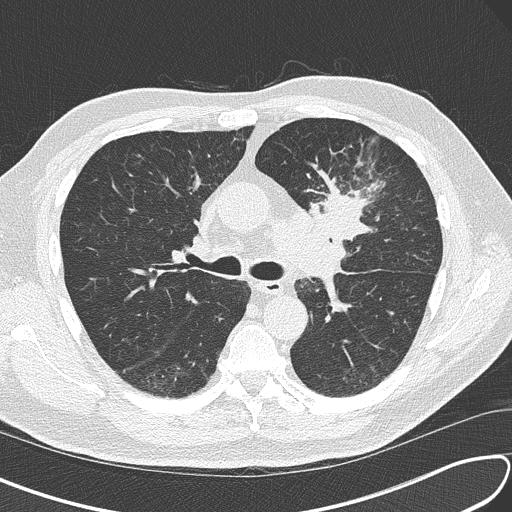
Axial slice from a low-dose chest CT screening exam, third screening round (two years after baseline), lung window (W 1500 / L -600 HU), 2 mm slice thickness. Male, age 67 years at enrolment. Current smoker at enrolment.
Lesion marked by an expert reader, bounding box <296,168,397,261> (left, top, right, bottom; pixels). Screening reader's record for this exam (one nodule recorded; not confirmed to be the boxed lesion): non-calcified nodule or mass ≥4 mm, left upper lobe, 30 × 23 mm, soft tissue attenuation, pre-existing on the prior screen: no. Official screen result: positive, other. Later outcome: lung cancer diagnosed 41 days after this screen — small cell carcinoma, NOS, left upper lobe, stage IV (AJCC 6th edition), 30 mm at pathology.